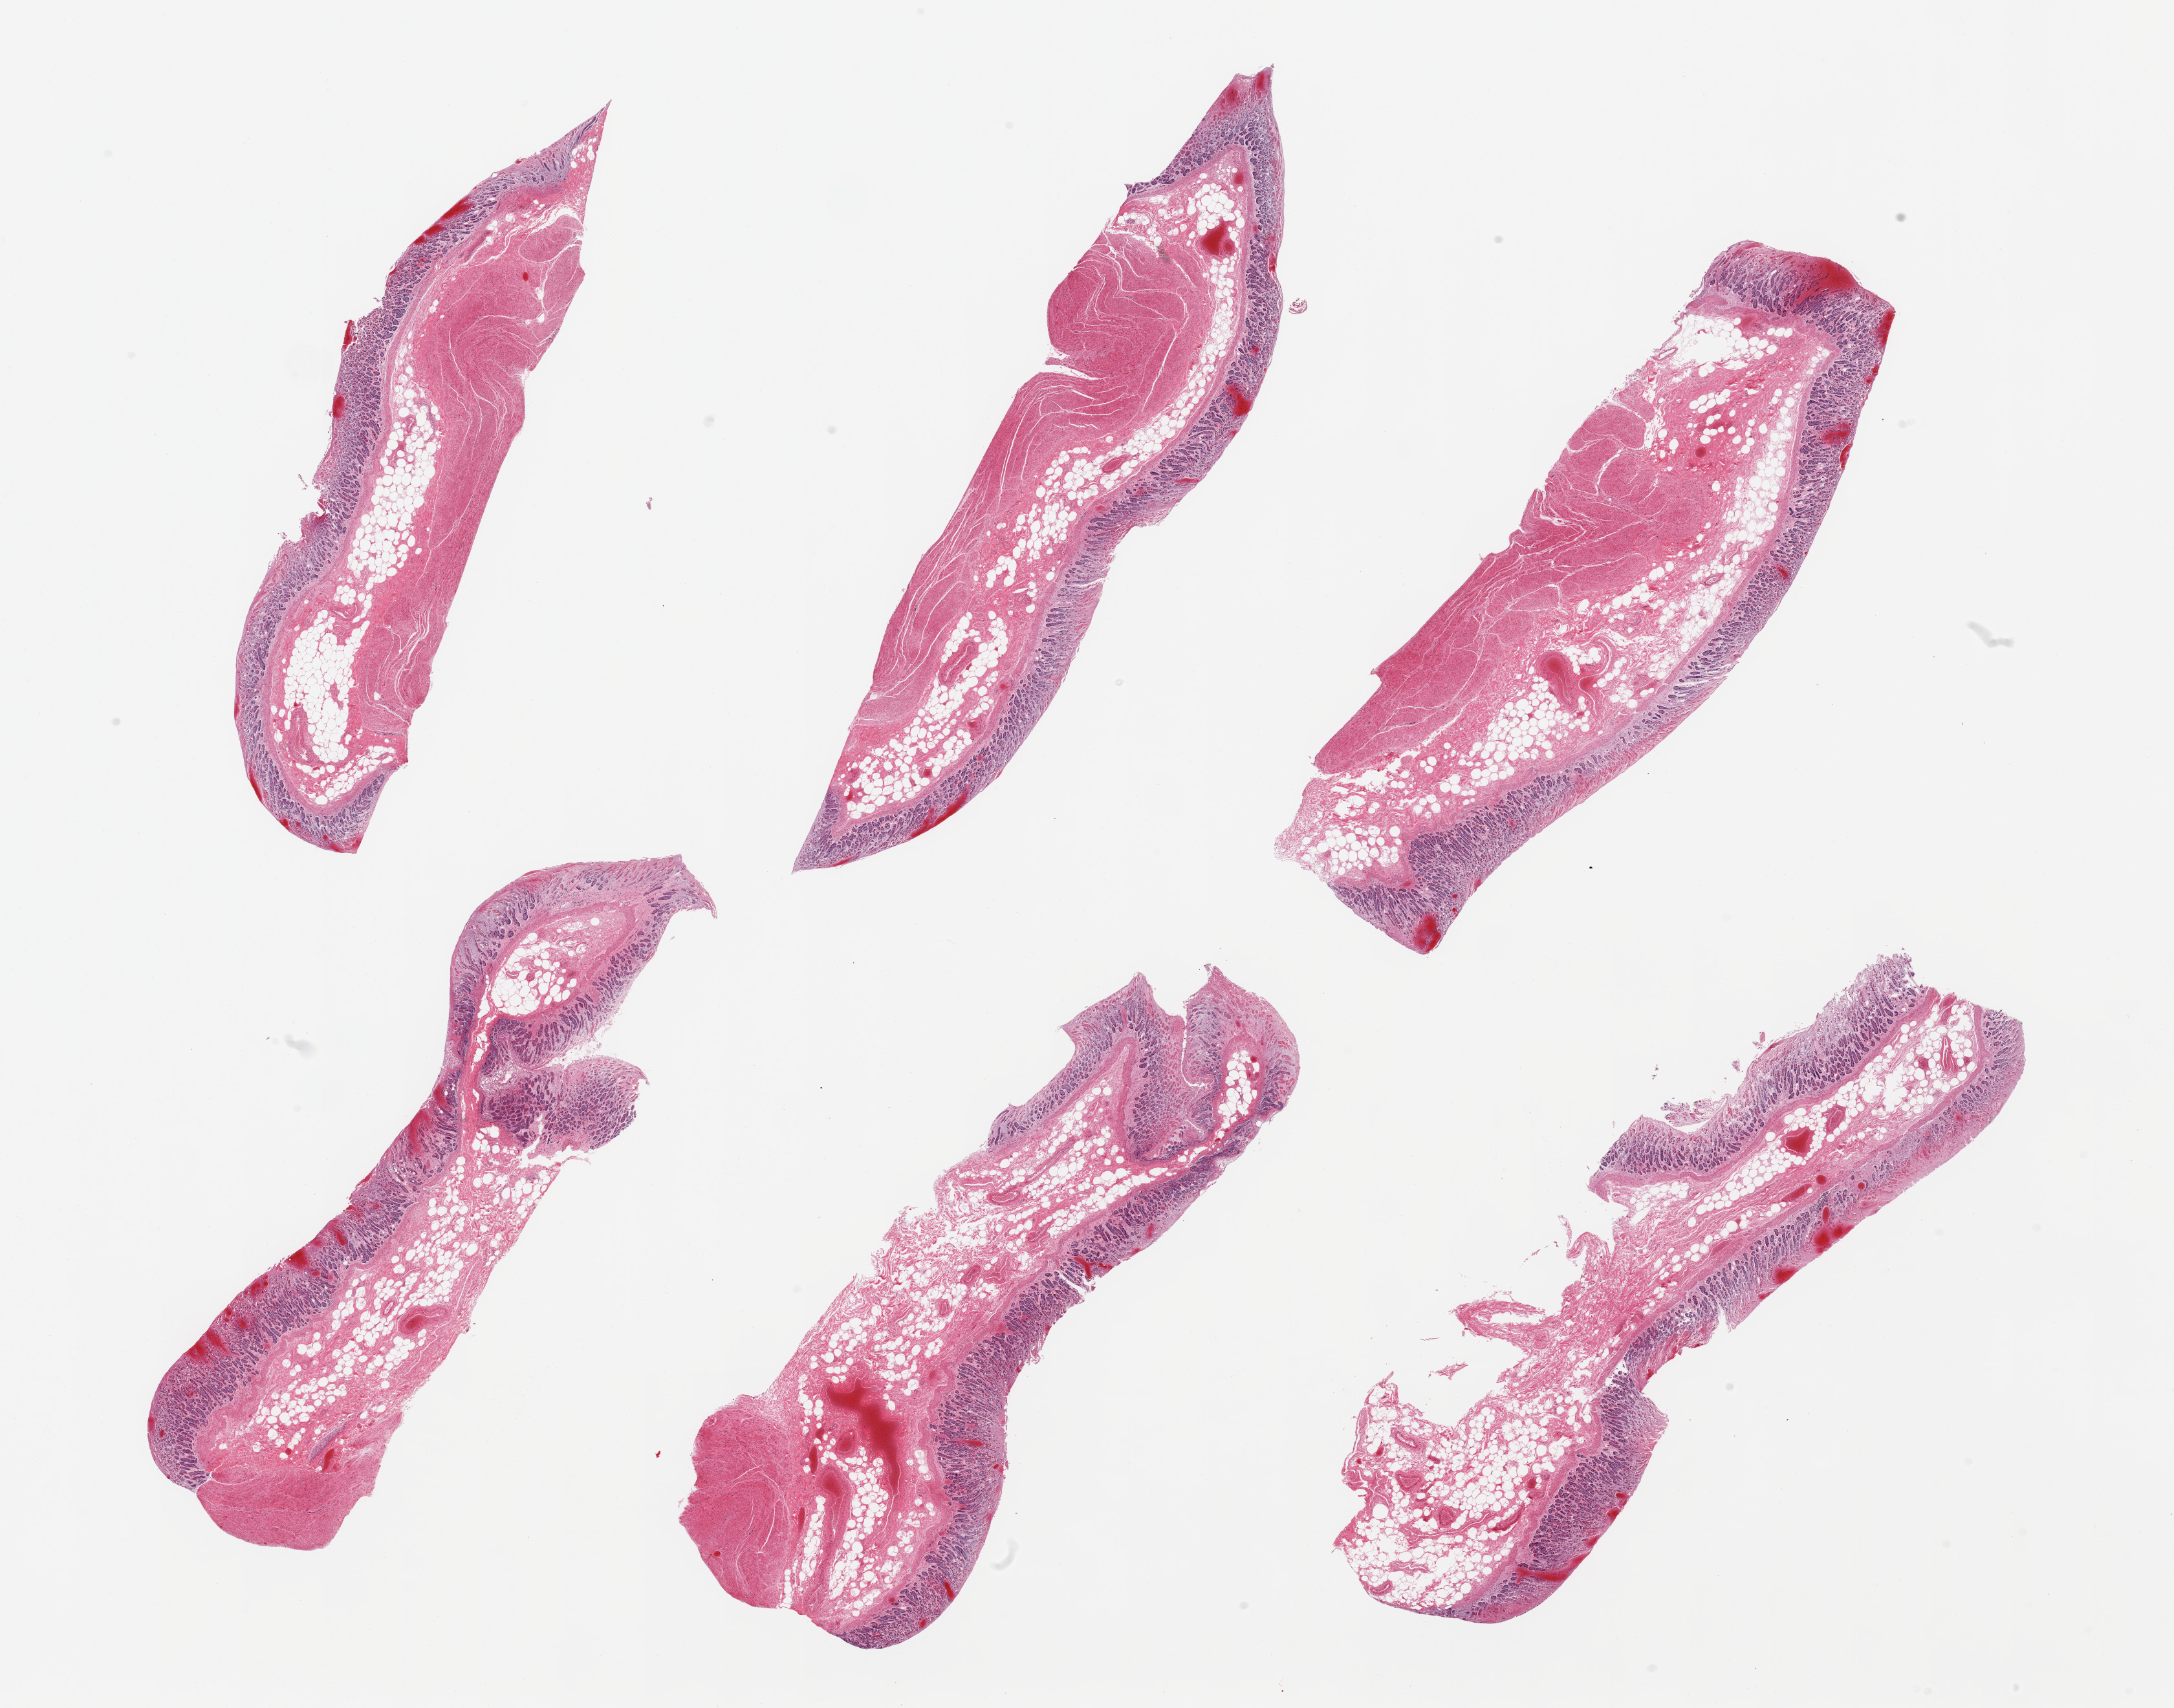
Whole-slide image, hematoxylin and eosin (H&E) stain, brightfield — shown as a low-resolution overview of the whole scanned area (about 26.6 x 20.9 mm), PAXgene-fixed paraffin-embedded (PFPE) section, sampled site (target tissue): stomach, donor tissue sample. Male donor.
Reviewer comment on this tissue sample: 6 pieces, mucosa up to ~0.4mm, ~20% thickness; moderately advanced autolysis.